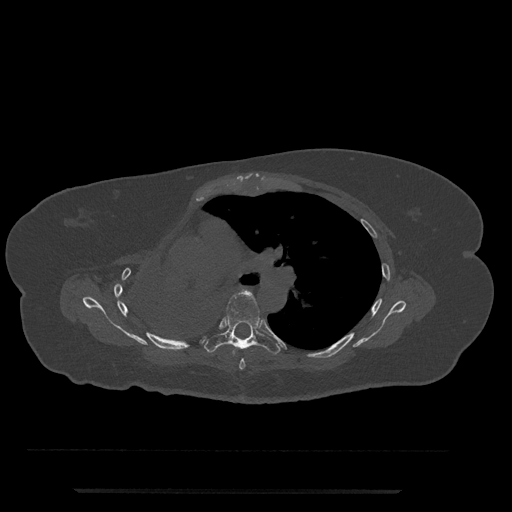
CT including the spine, one axial slice; slice 505 of 797 in the series (ordered by position); reconstruction kernel Br40s/3; bone window (W 1800 / L 400 HU); 512 × 512 image matrix, field of view 440 × 440 mm. Patient: female, 51 years. Case-level facts recorded for this patient, not image findings: primary cancer: neuro; vertebrae with lytic lesions (as recorded): T8.
Outlined on this slice (semi-automatic segmentation, software-assisted and operator-edited):
- T5 vertebra: bounding box [x1, y1, x2, y2] px = [239, 337, 277, 370]
- T6 vertebra: [206, 291, 280, 357]